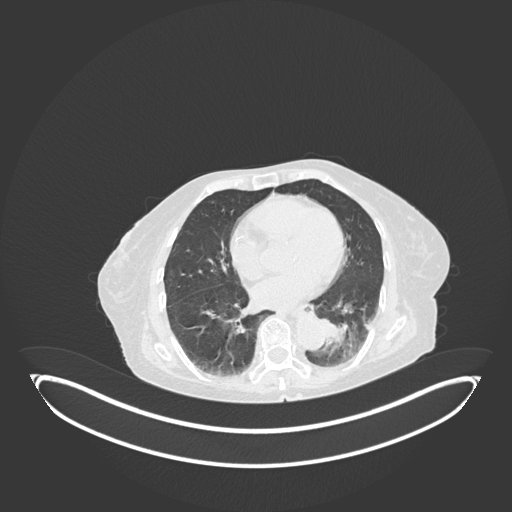
Chest CT, one axial slice; position 41 of 189 along the scan axis; reconstruction kernel B30f; lung window (W 1500 / L -600 HU); 1 mm slice thickness; 512 × 512 image matrix, field of view 500 × 500 mm. Patient: female, 82 years. From the clinical record (not read from this slice): clinical TNM (as recorded): T1b N0 M1.
Structures marked on this image (rectangle marked by the reading radiologist):
- lung tumour (recorded histology: adenocarcinoma): box from (x=318, y=313) to (x=350, y=351) px